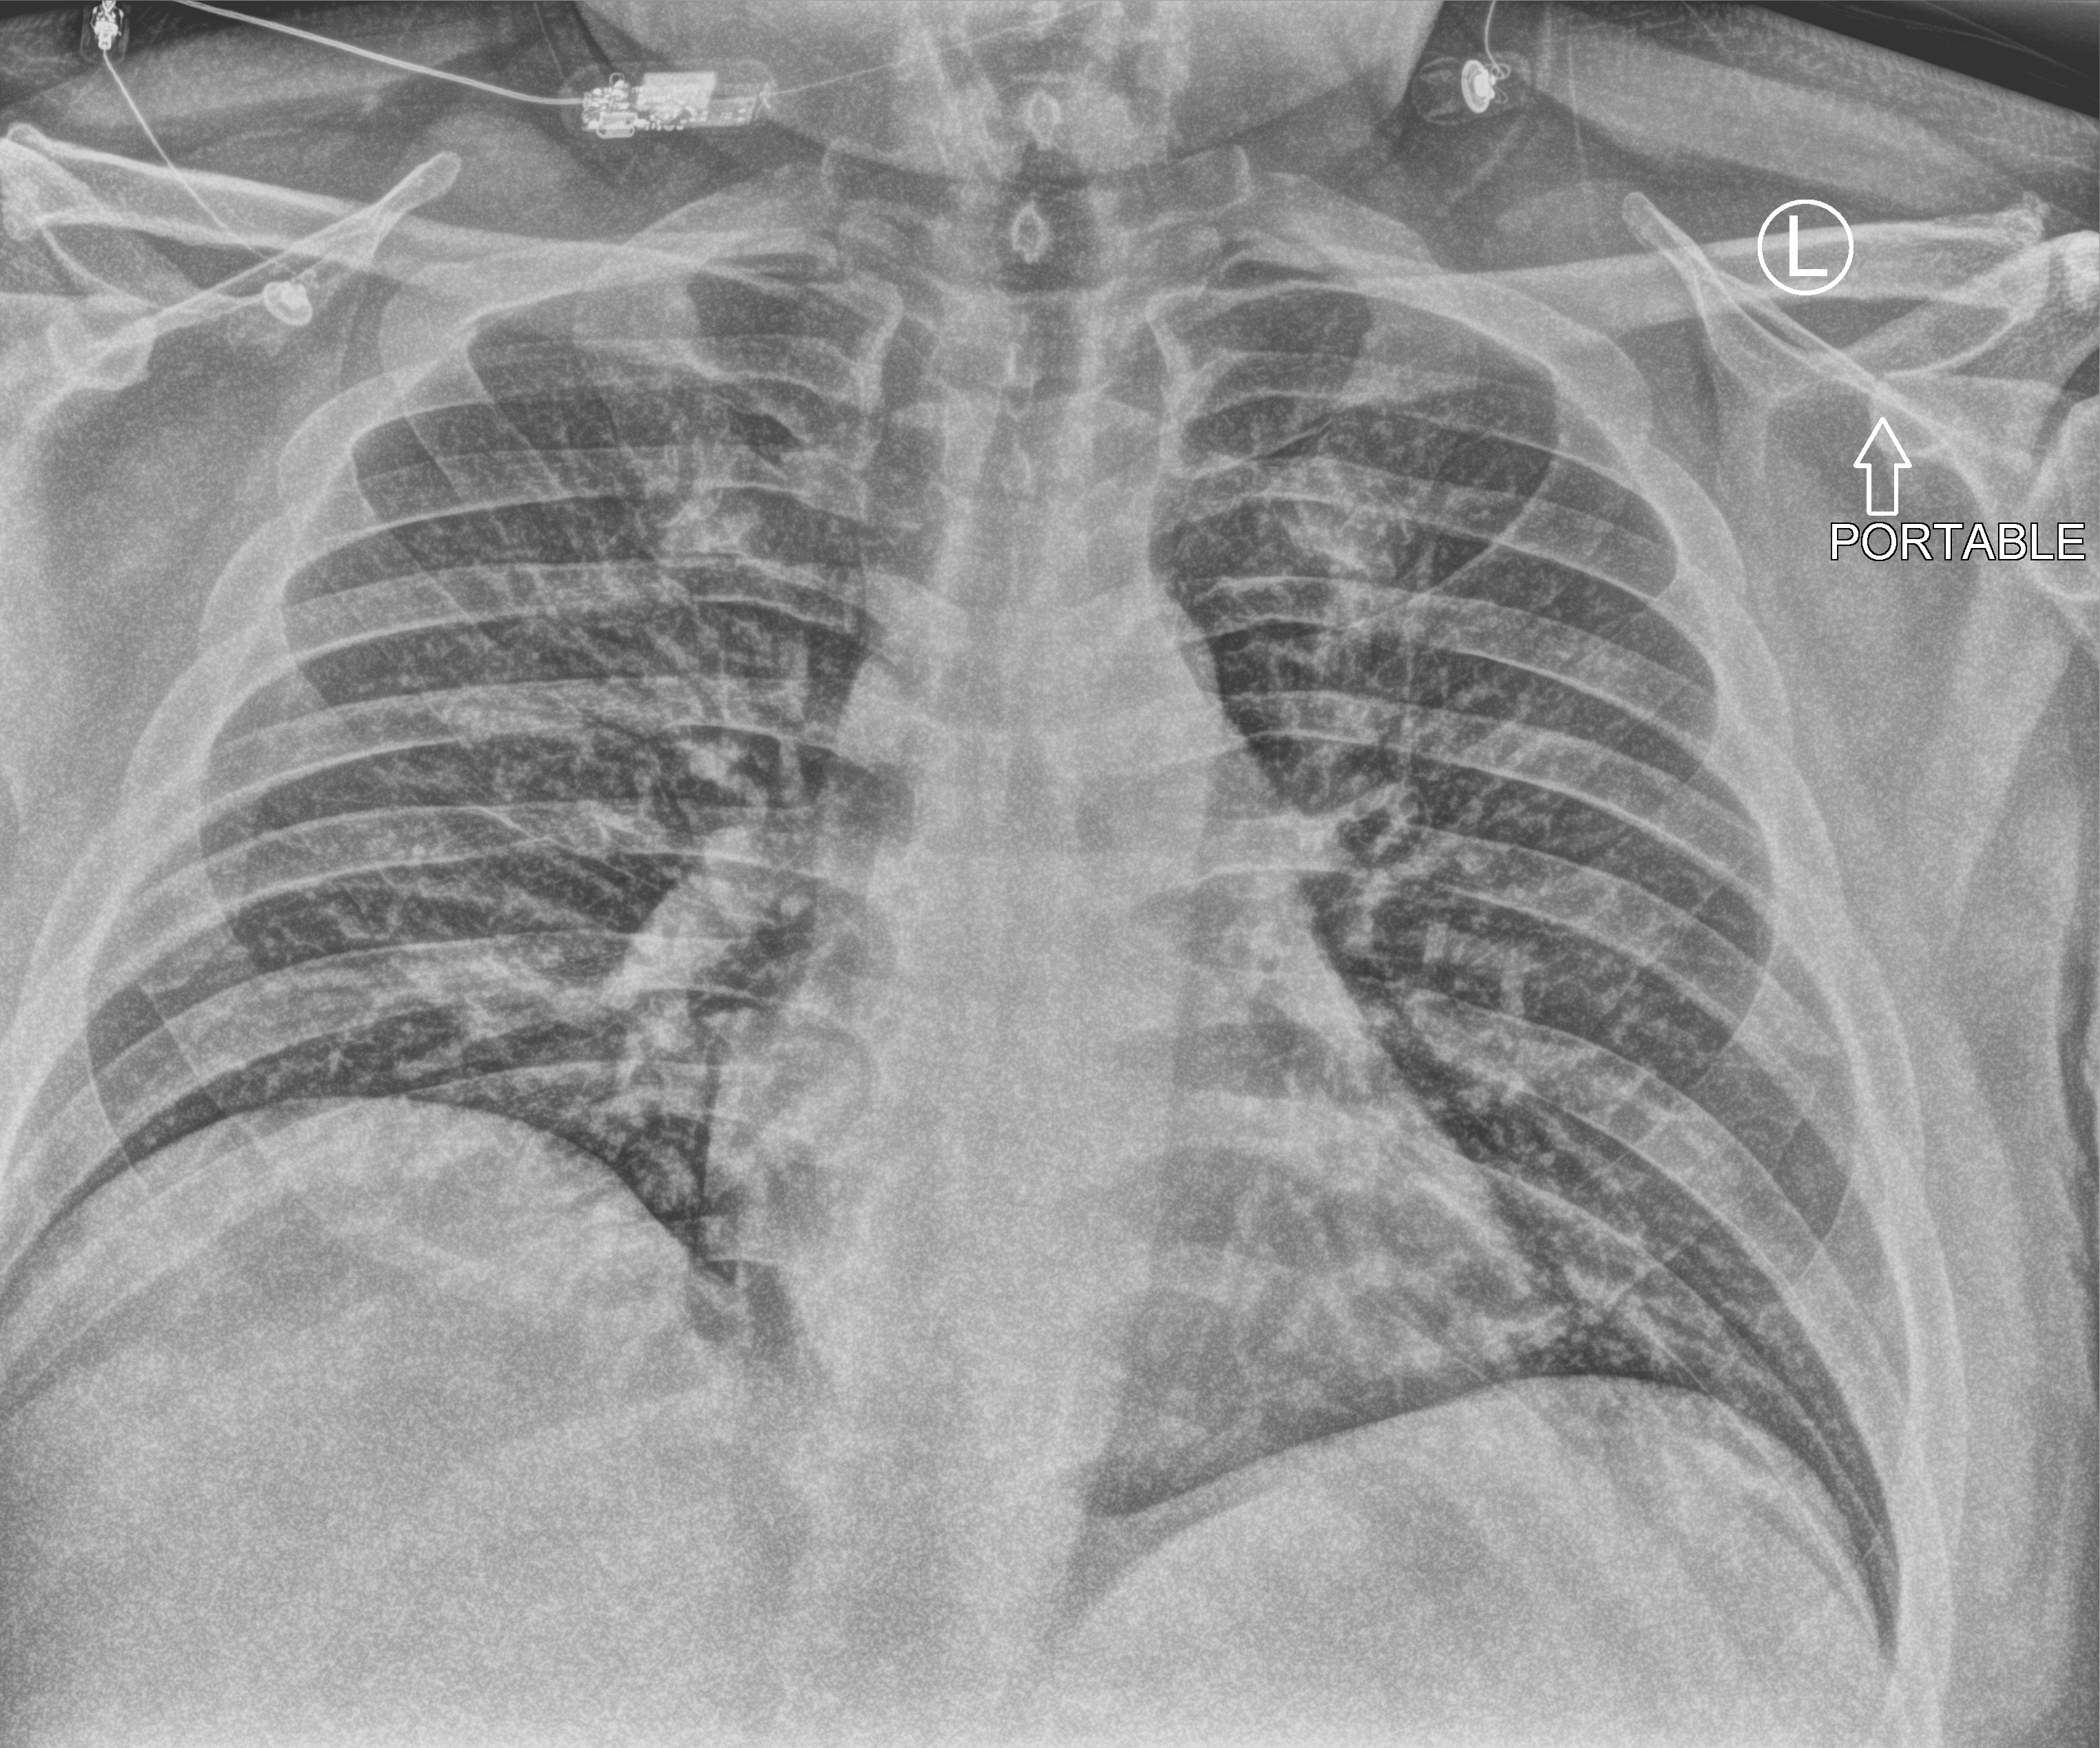
Portable chest radiograph, anteroposterior (AP) projection. Patient hospitalised with COVID-19; male, aged 18–59 years.
Admission-level facts for this patient (not findings on this image; timing relative to this image not recorded):
- admitted to intensive care during this hospital stay: no